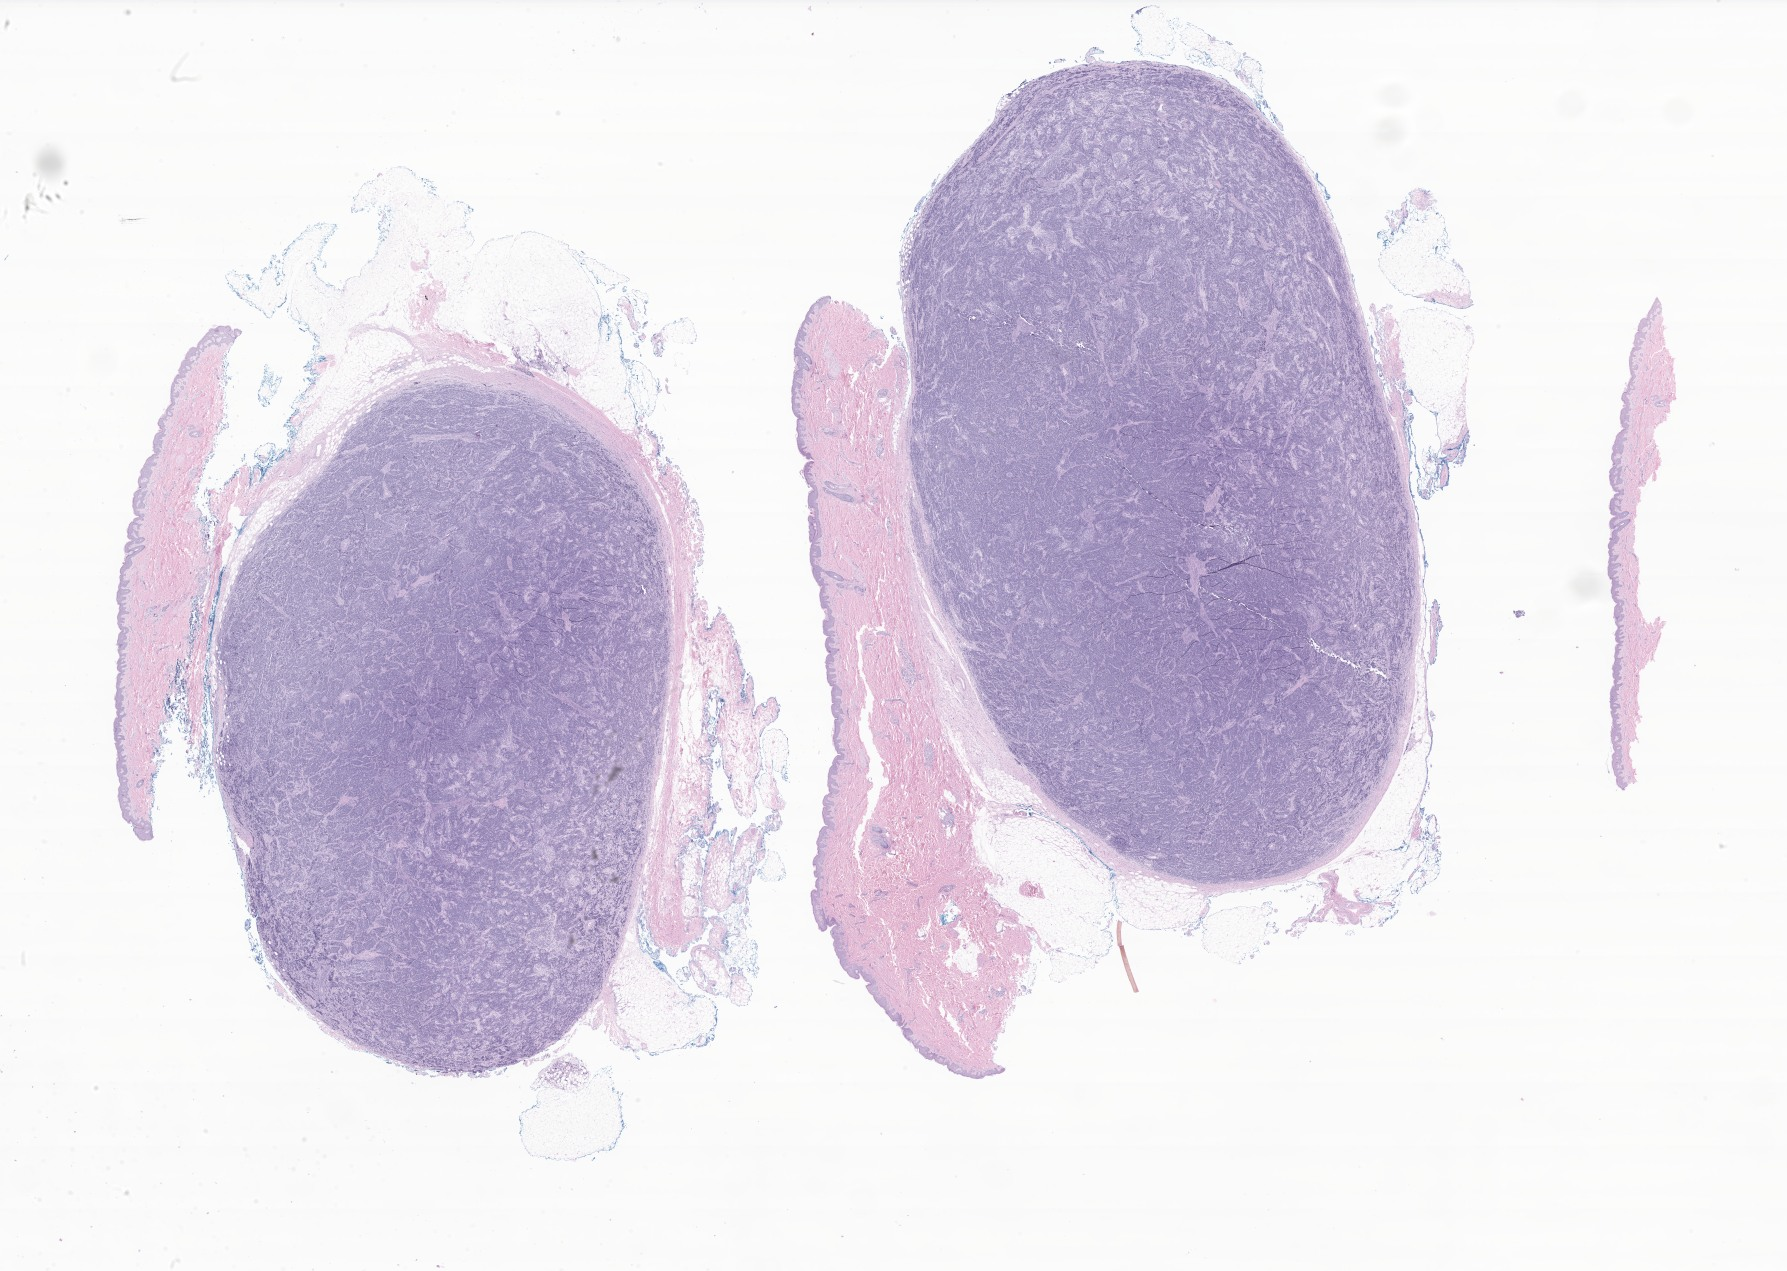
Digitized hematoxylin and eosin (H&E)-stained section of tumor tissue from the skin of trunk — shown as a low-resolution overview of the whole scanned area (about 30.1 x 21.4 mm); FFPE section. Patient female; age 195 days.
Diagnosis: Neuroblastoma, NOS.